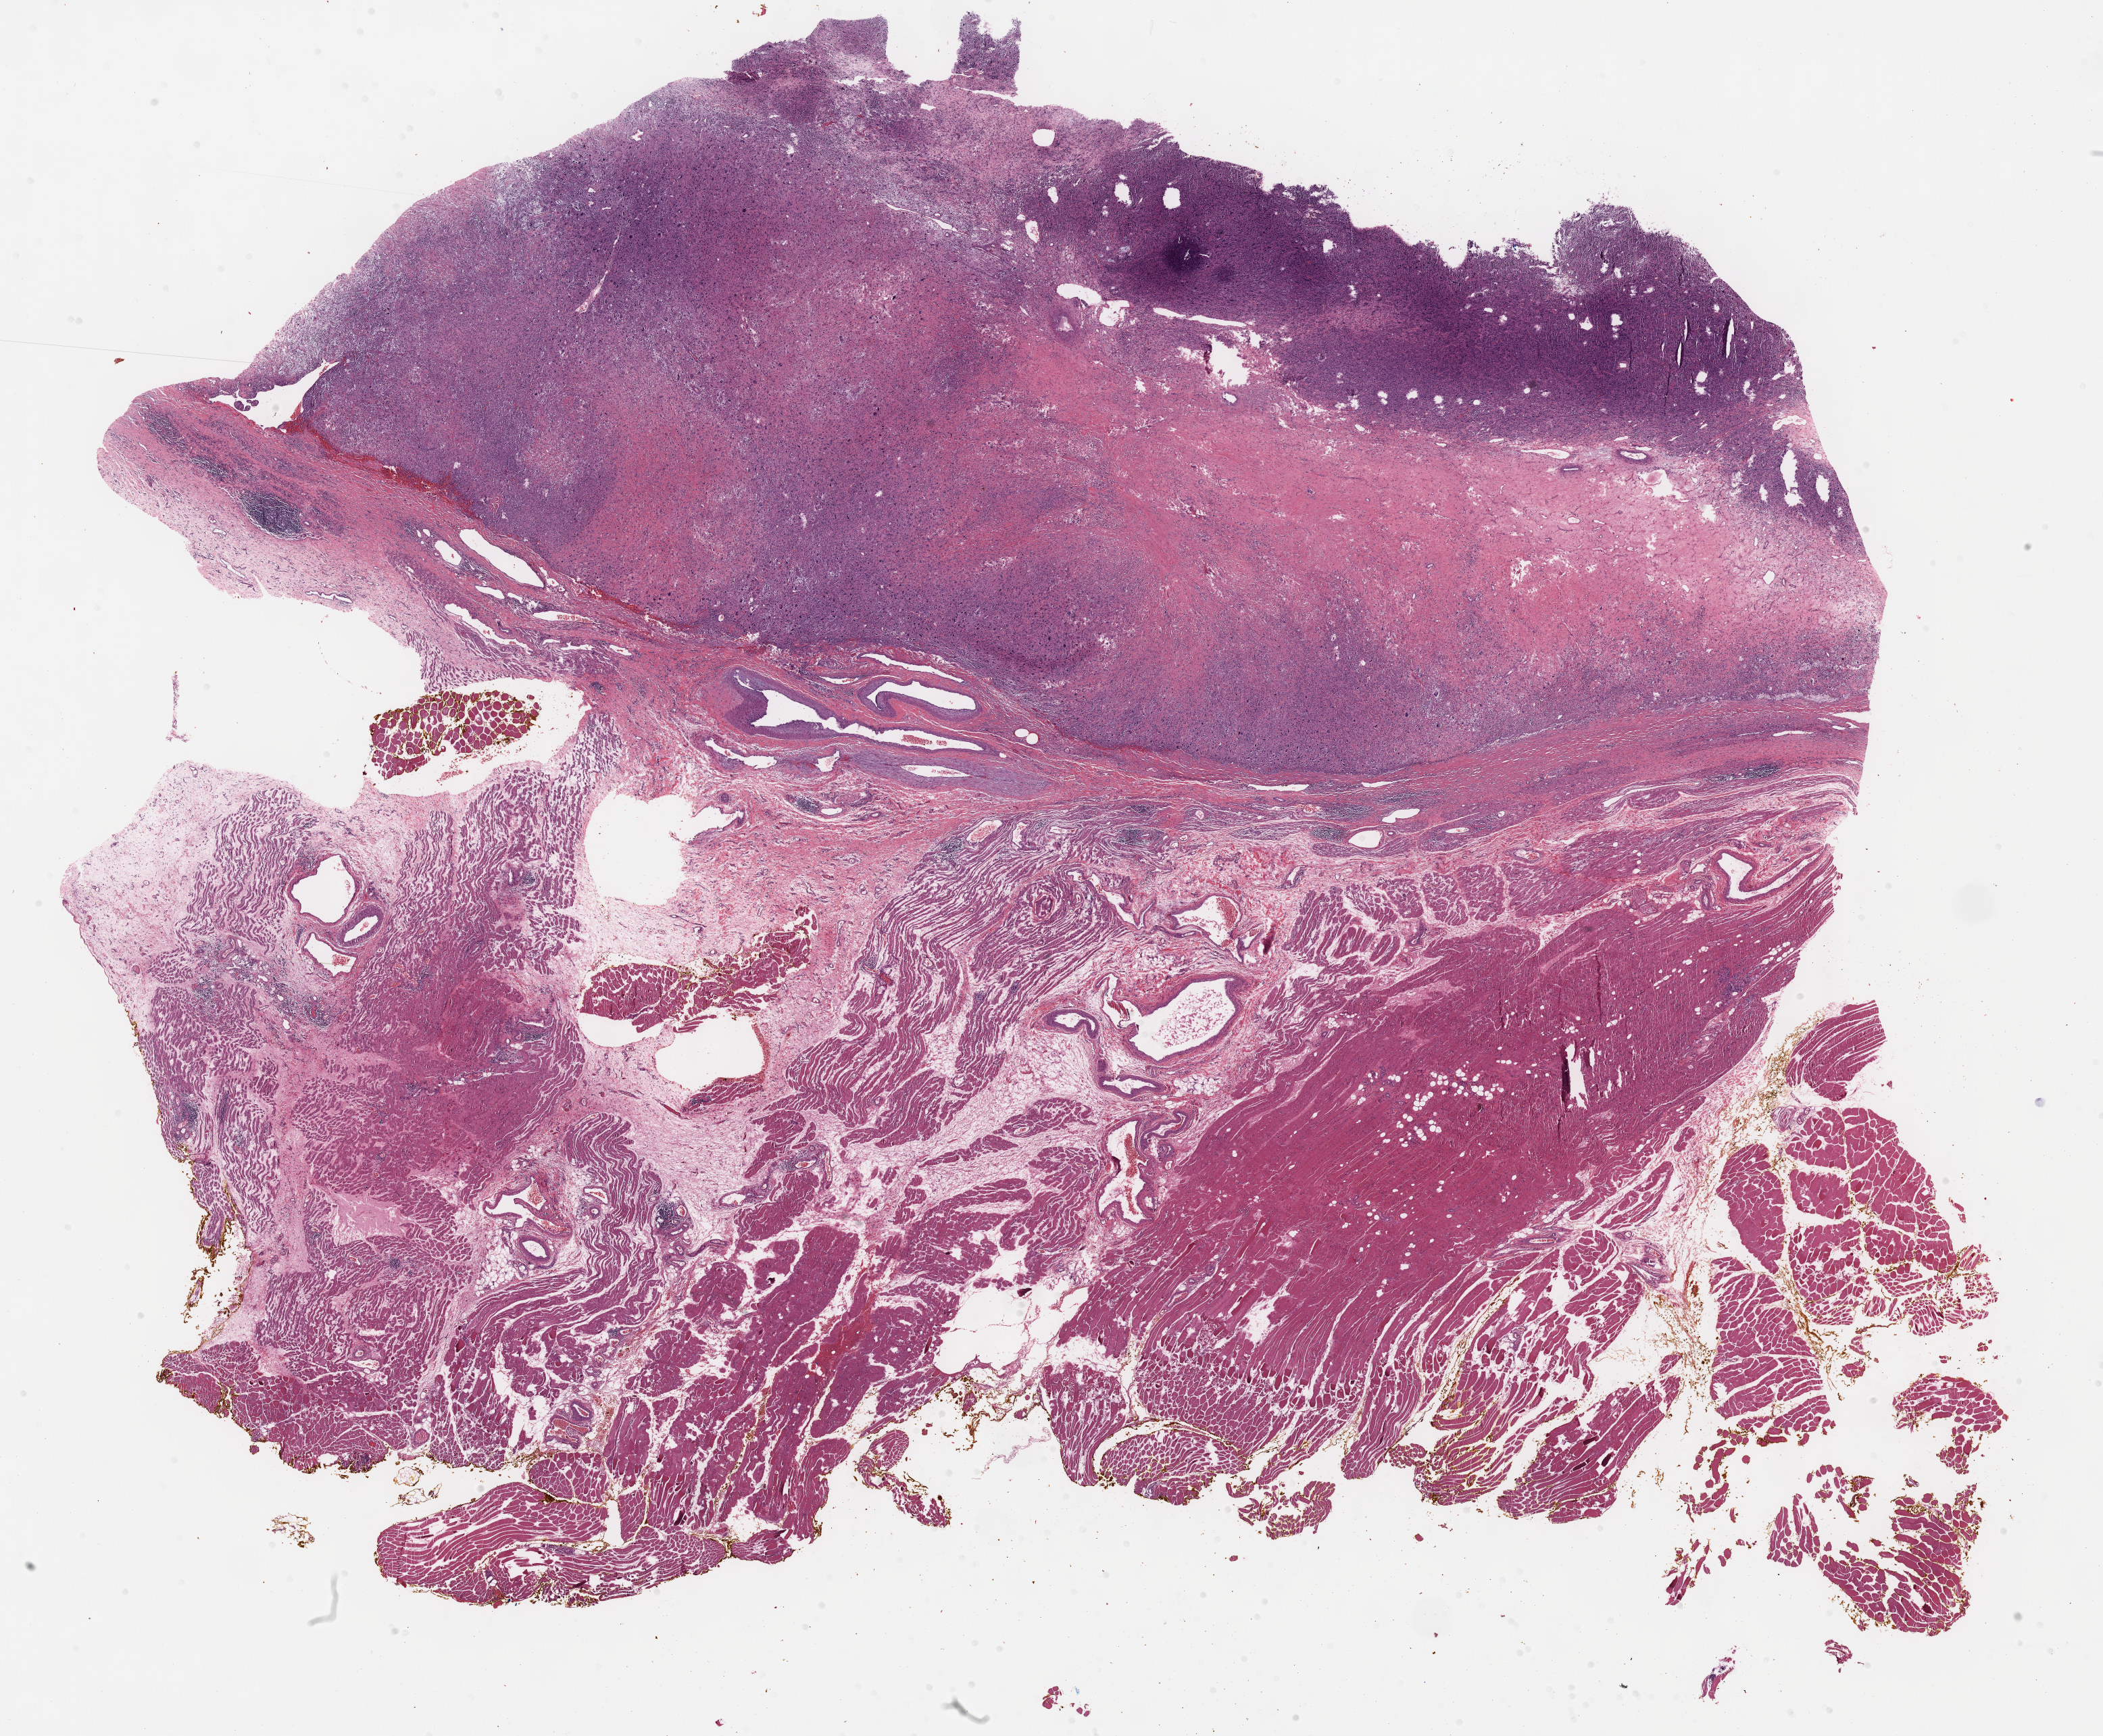
Digitized H&E tissue section (whole slide), low-resolution overview of the scanned area, about 25.2 x 20.8 mm (from a 40x scan); formalin-fixed paraffin-embedded (FFPE) diagnostic section; sample: primary tumour, connective, subcutaneous and other soft tissues. Patient: male, age at initial diagnosis 51 years.
Histologic diagnosis: Fibromyxosarcoma (connective, subcutaneous and other soft tissues of thorax).